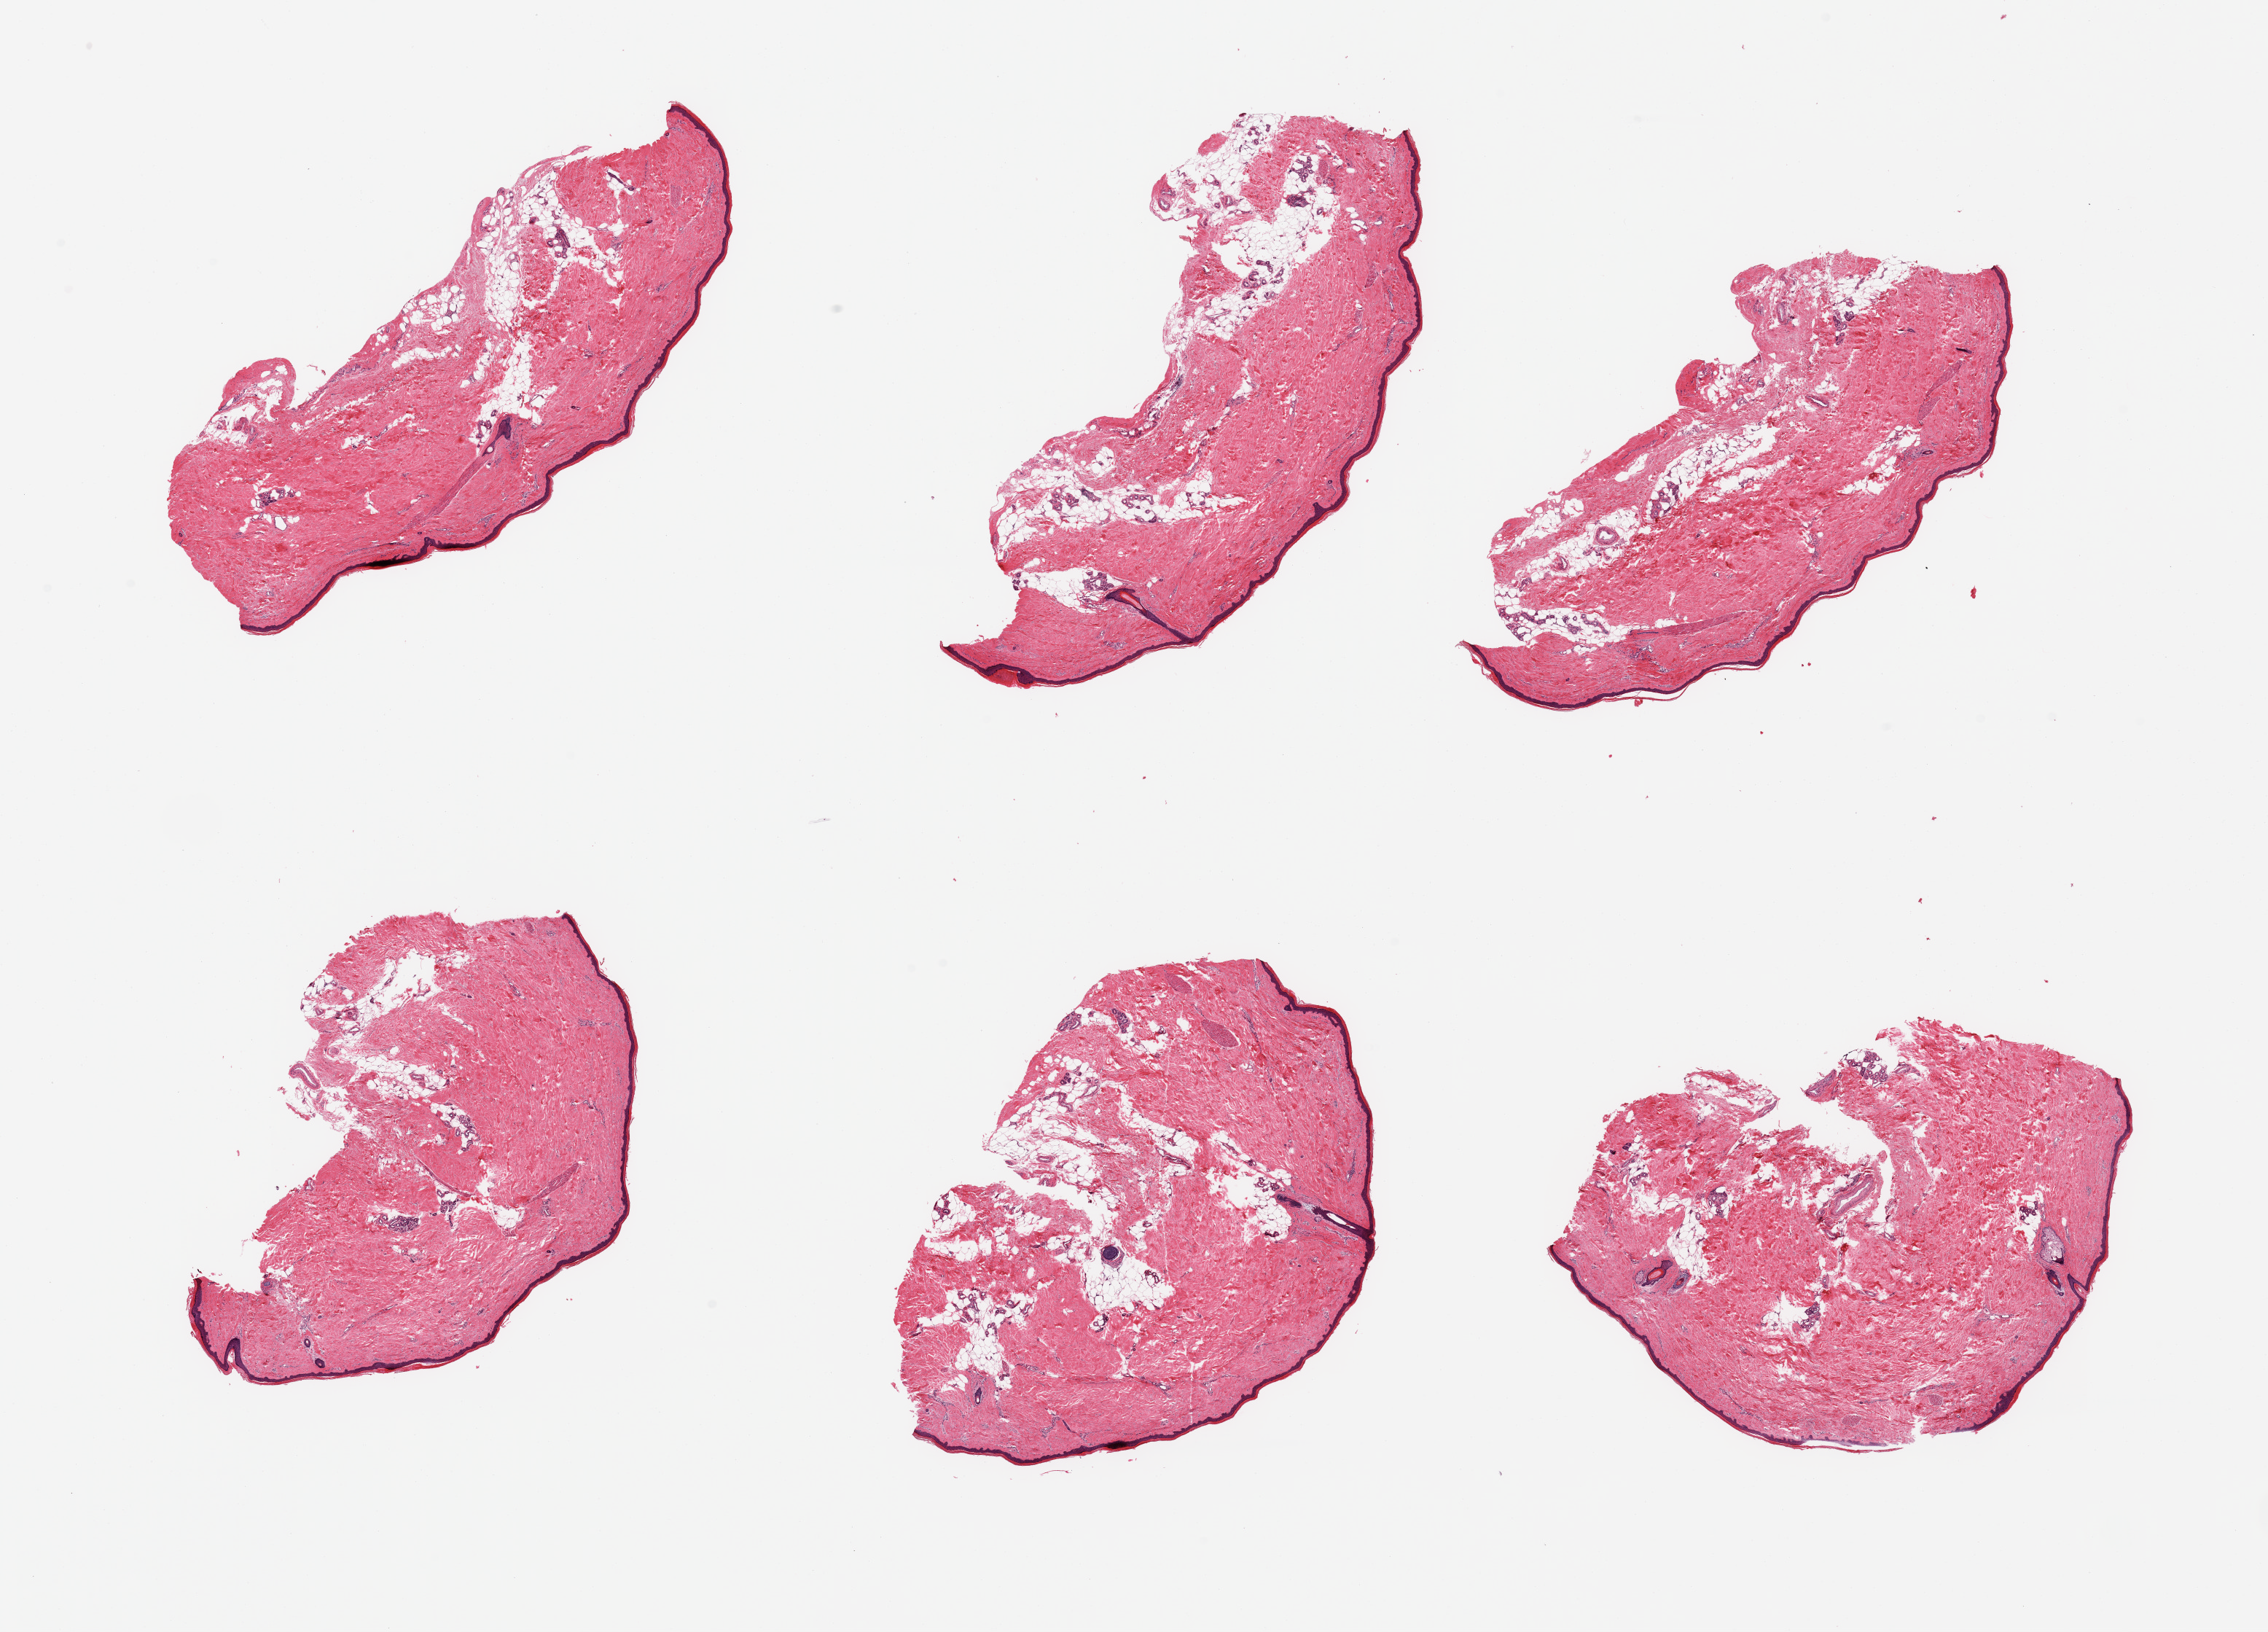
Hematoxylin and eosin (H&E) whole-slide image, a low-resolution overview of the entire scanned area, about 24.6 x 17.7 mm. PAXgene-fixed paraffin-embedded (PFPE) section. Target tissue: skin of lower leg. Tissue donor sample.
Review note (as recorded): 6 pieces; include from 10-20% mostly internal fat, epidermis measures 38 microns.